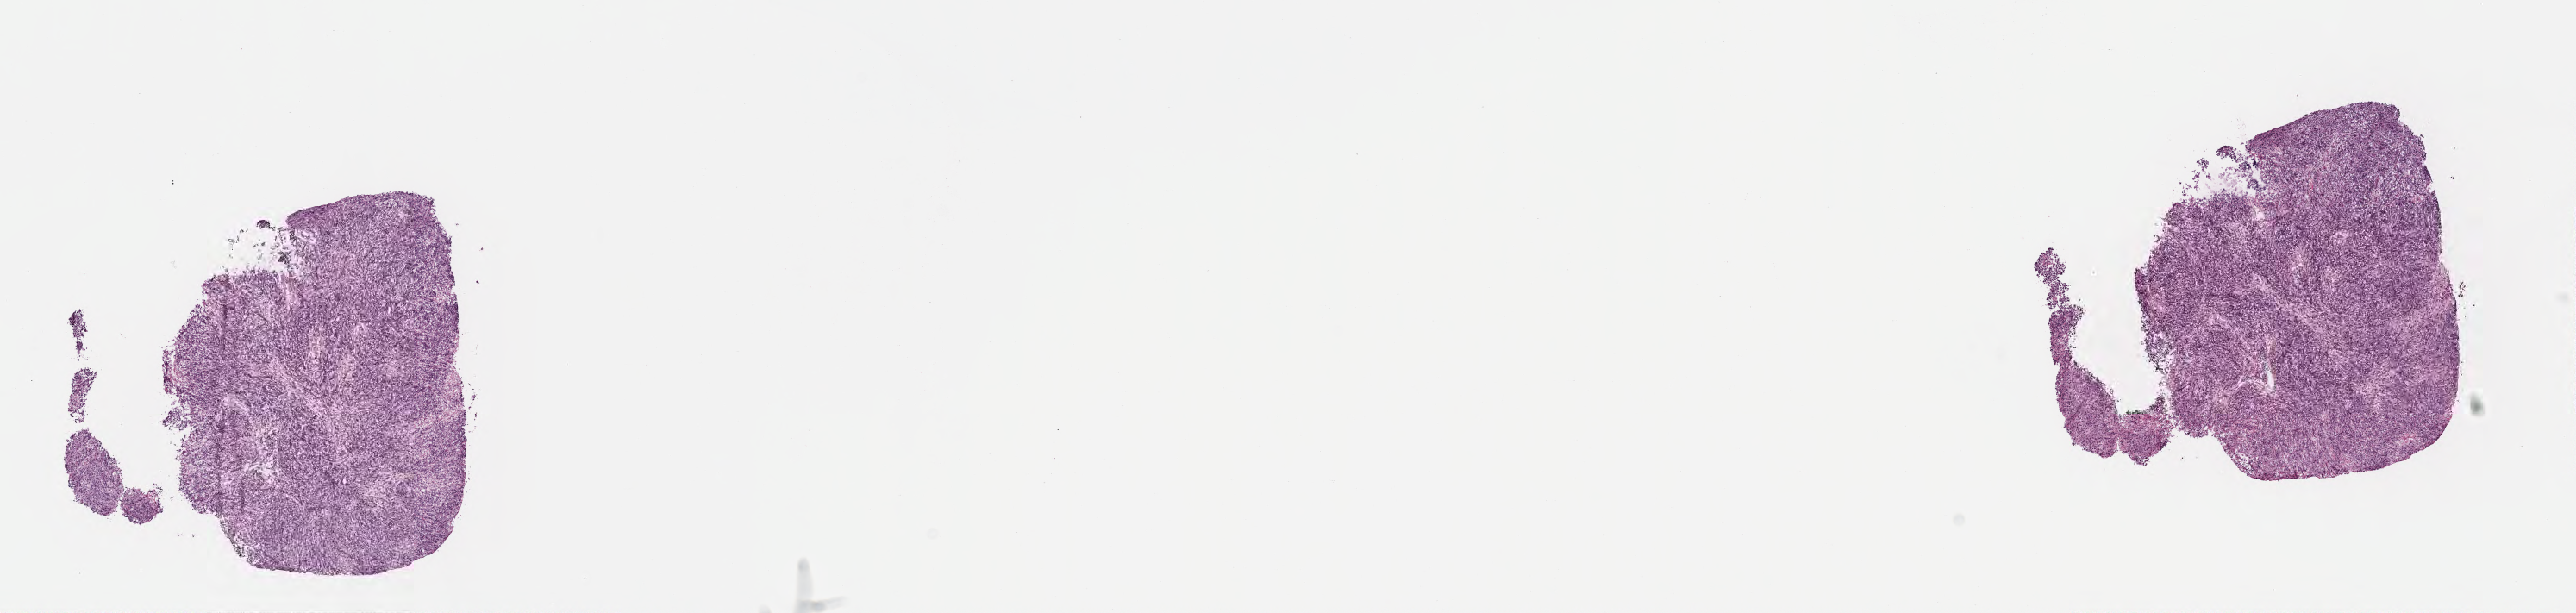
Whole-slide image, hematoxylin and eosin (H&E) stain — a low-resolution overview of the entire scanned area, about 24.1 x 5.7 mm. Cryosection. Metastatic tumor tissue, resected from lymph node. Patient: male, age at initial diagnosis 70 years. Slide review estimates, as recorded: tumor cells 90%, tumor nuclei 90%, stromal cells 10%, necrosis 0%, normal cells 0%. Infiltration values recorded for this section: lymphocyte infiltration 3%, monocyte infiltration 1%, neutrophil infiltration 3%.
Patient diagnosis (primary): Carcinoma, NOS.